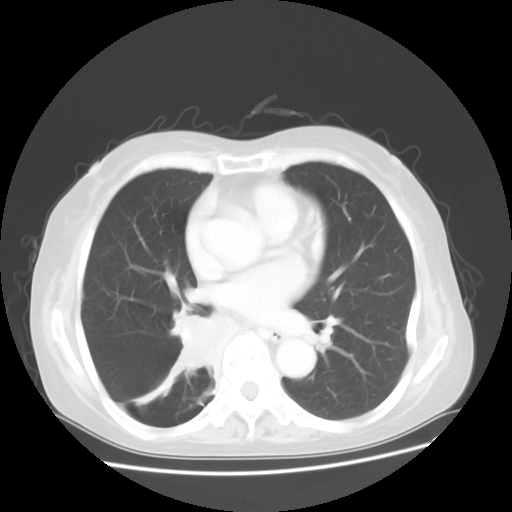
Chest CT, one axial slice. Slice 22 of 48 in the series (ordered by position). Reconstruction kernel STANDARD. 120 kVp. Lung window (W 1500 / L -600 HU). 5 mm slice thickness. 512 × 512 image matrix. Patient: female, 63 years. From the clinical record (not read from this slice): clinical TNM (as recorded): T2 N3 M1b.
Annotated regions visible in this slice (bounding box drawn by a radiologist):
- lung tumour (recorded histology: small cell carcinoma): box from (x=172, y=310) to (x=217, y=383) px